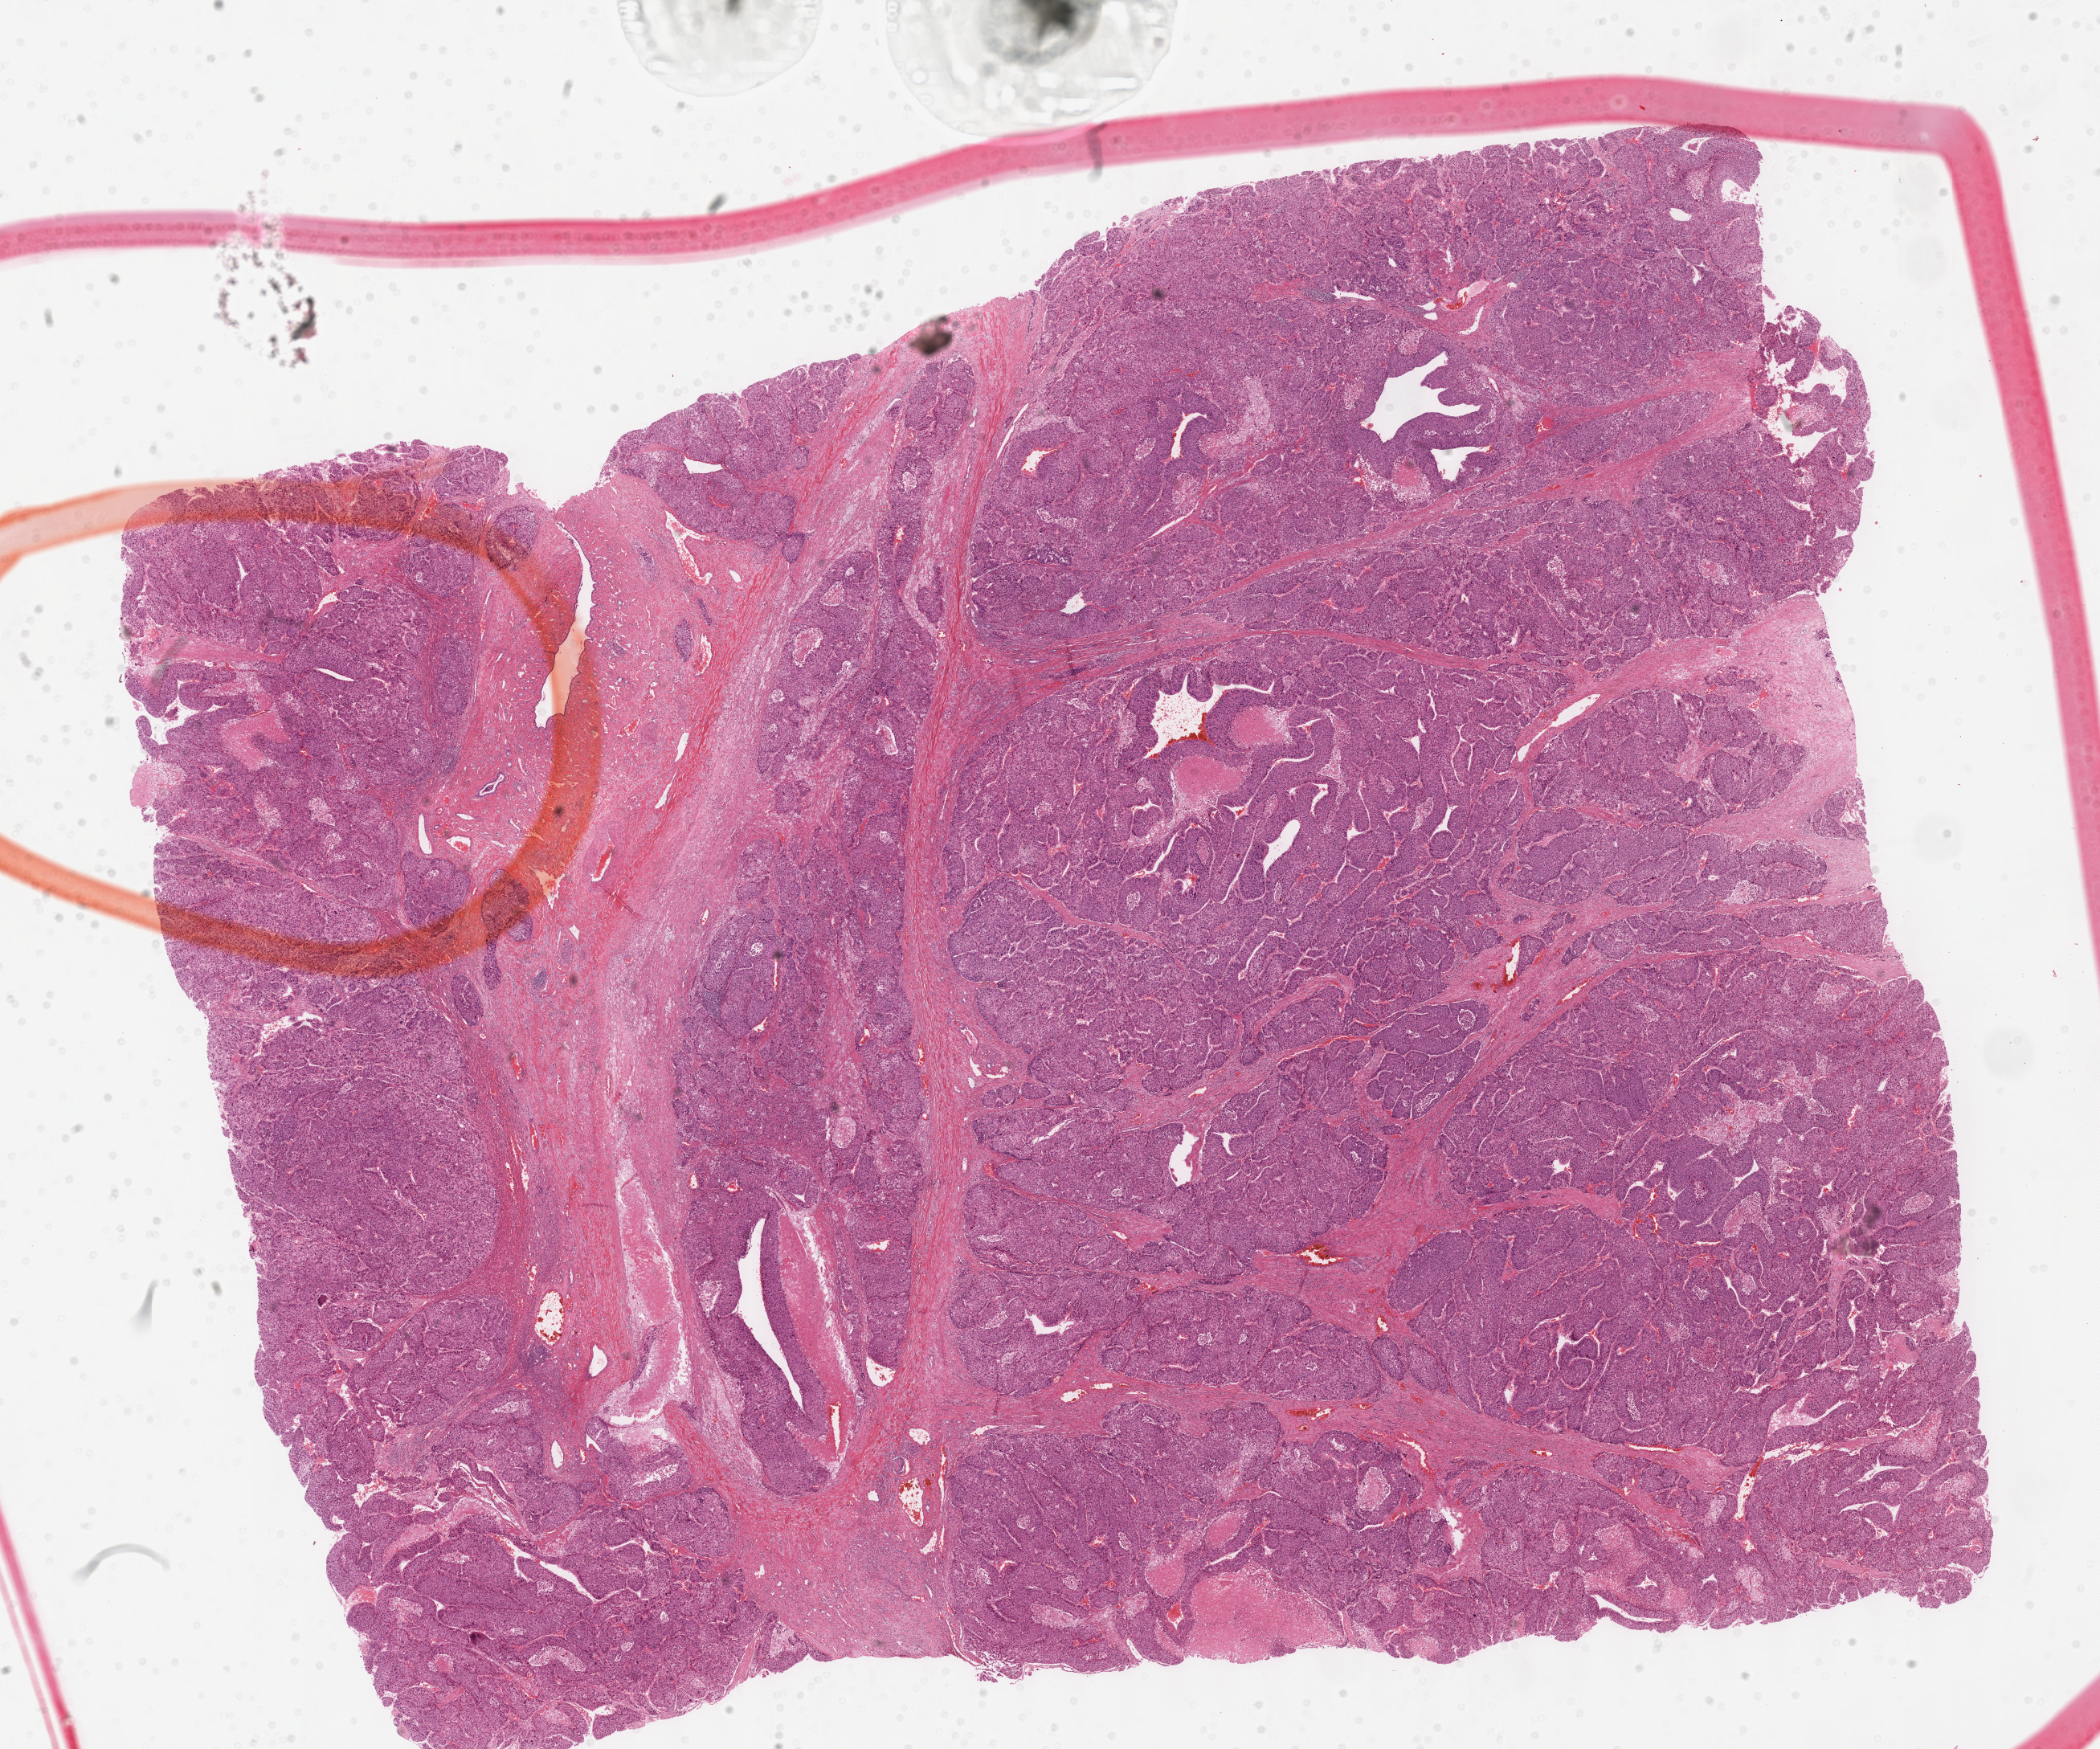
Hematoxylin and eosin (H&E) stained whole-slide image — shown as a low-resolution overview of the whole scanned area (about 21.1 x 17.6 mm, acquisition: 40x scan). Formalin-fixed paraffin-embedded (FFPE) diagnostic section. Sample: primary tumour, liver. Patient: female, age at initial diagnosis 50 years. Histologic grade: G3 (poorly differentiated).
Pathologic diagnosis: Hepatocellular carcinoma, NOS. TNM: T3a N0 M0. AJCC pathologic stage: IIIA.